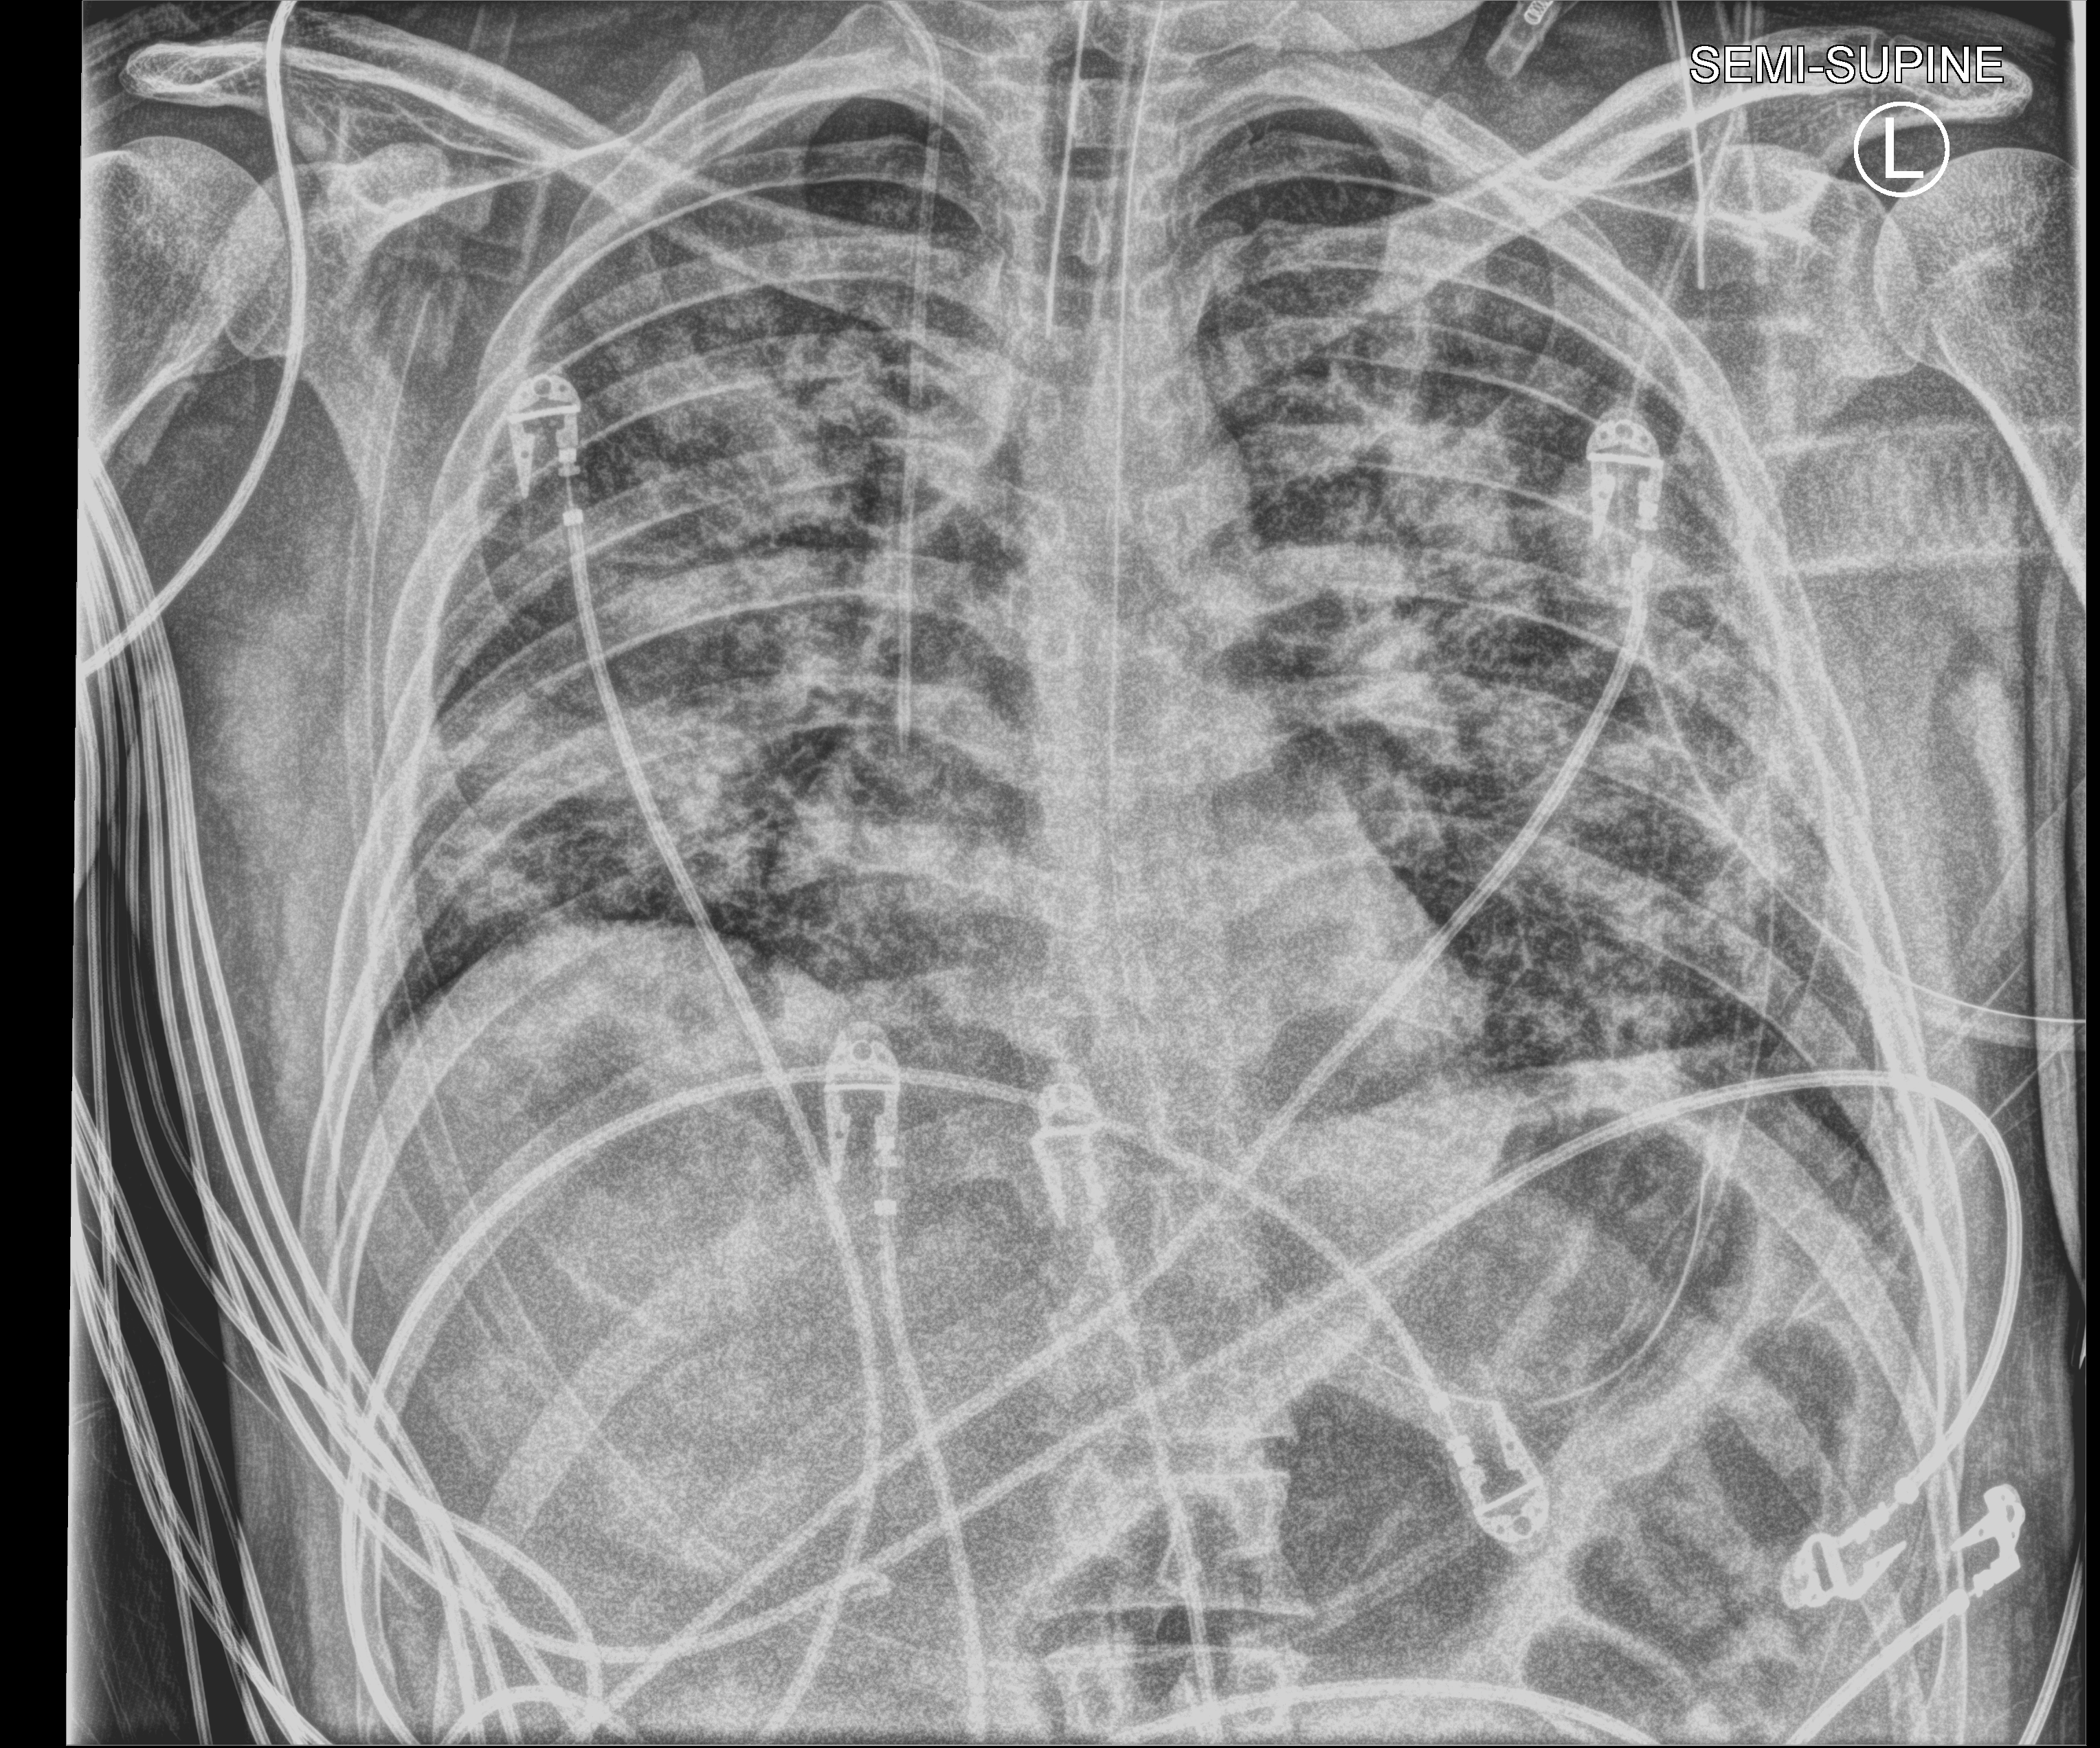
Portable chest radiograph. Male patient hospitalised with COVID-19, age 18–59 years.
From the hospital-stay record, not from the radiograph (when in the stay this image was taken is not recorded): diabetes (admission record): no; mechanically ventilated during this hospital stay: yes.